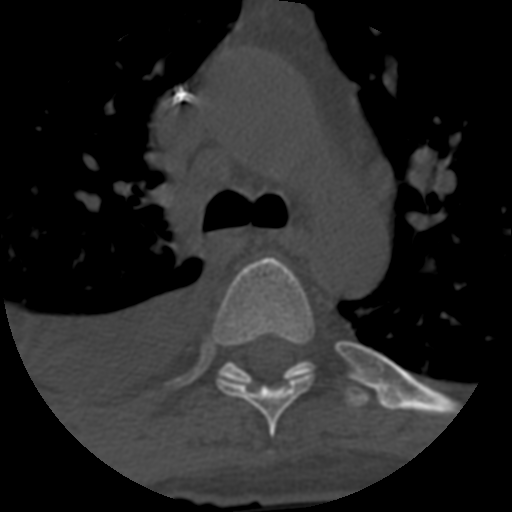
CT including the spine, one axial slice. Slice 448 of 708 in the series (ordered by position). 120 kVp. One of 3 acquisitions stored at this slice position. Bone window (W 1800 / L 400 HU). 512 × 512 image matrix. Patient age 55 years. Case-level facts recorded for this patient, not image findings: primary cancer: colon; vertebrae with lytic lesions (as recorded): T12, L1, L5.
Annotated regions visible in this slice (semi-automatic segmentation, software-assisted and operator-edited):
- T5 vertebra: bounding box [x1, y1, x2, y2] px = [214, 257, 314, 437]
- T6 vertebra: [219, 361, 369, 409]